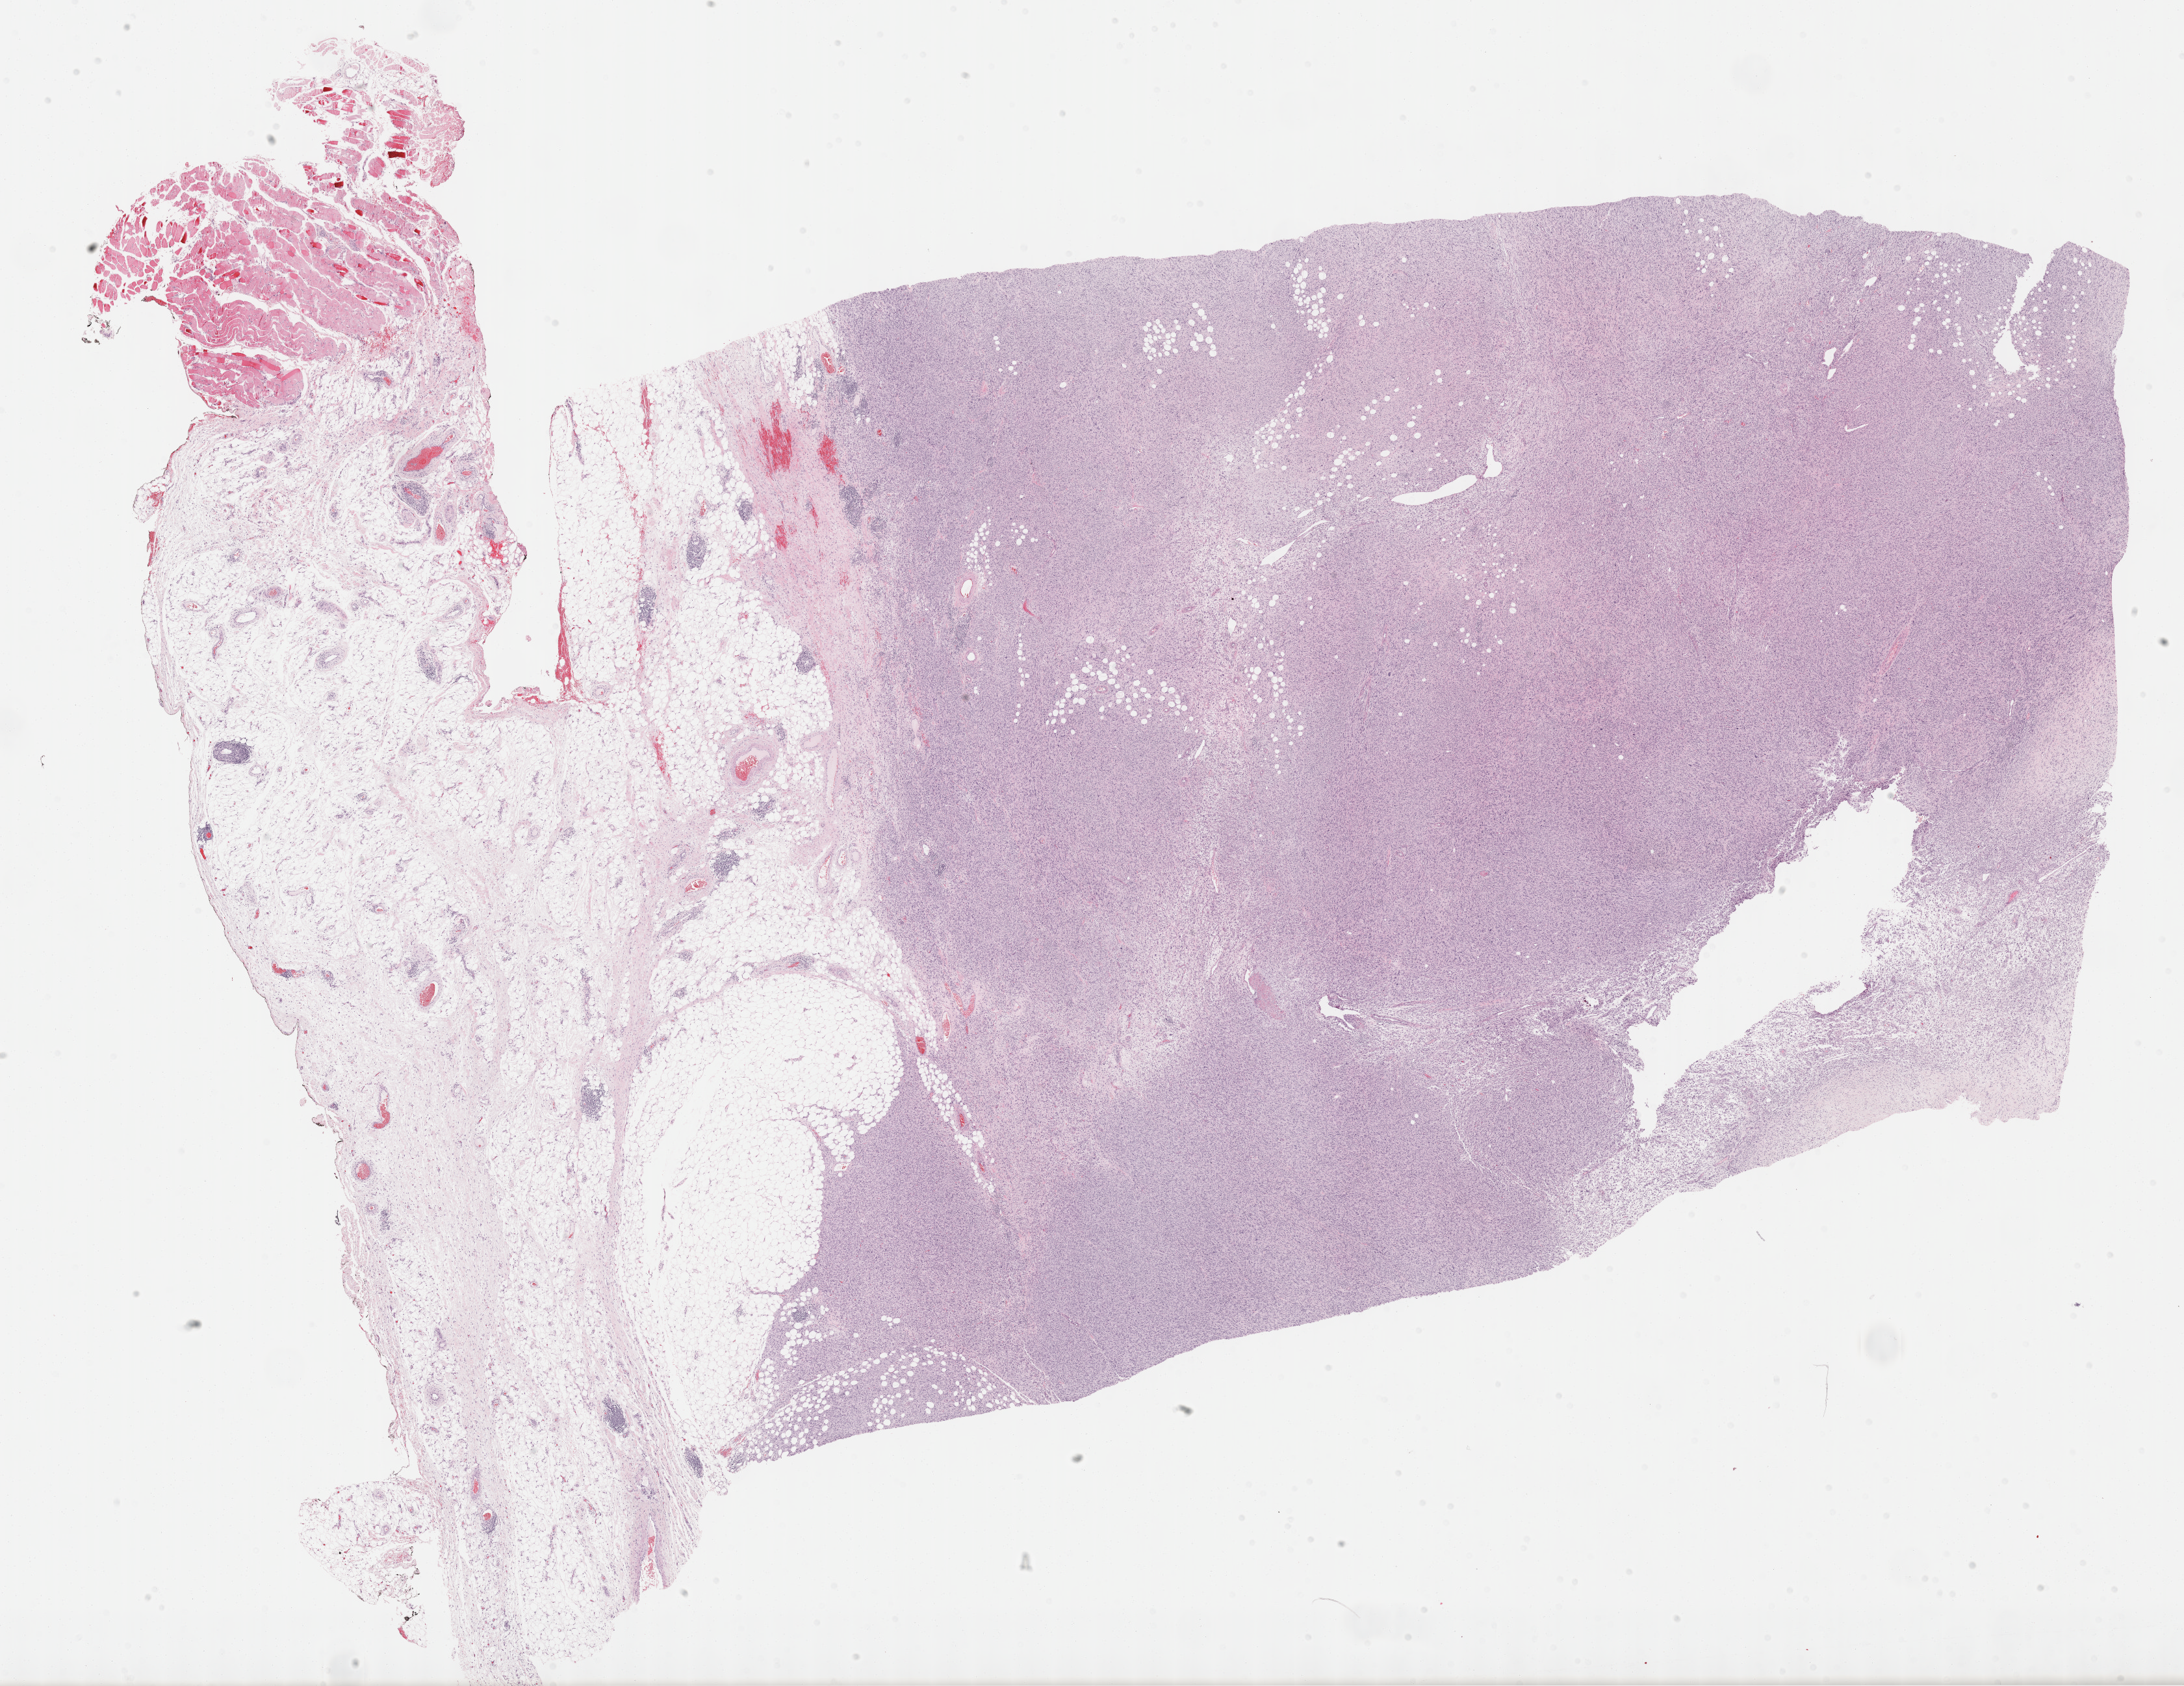
Digitized H&E-stained tissue section (whole slide), shown as a low-resolution overview of the whole scanned area (about 27.2 x 21.0 mm), formalin-fixed paraffin-embedded (FFPE) diagnostic section, connective, subcutaneous and other soft tissues, primary tumour sample. Patient: female, age at initial diagnosis 63 years.
Pathologic diagnosis: Malignant fibrous histiocytoma.